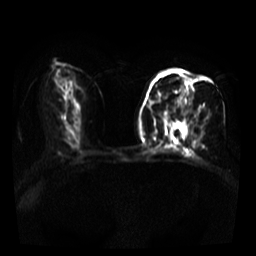
Breast MRI, one axial slice; slice 17 of 39 in the series (ordered by position); diffusion-weighted series; image 2 of 4 stored at this slice position (different b-values; order by instance number); 3 T; 5 mm slice thickness; 256 × 256 image matrix, field of view 320 × 320 mm. Female patient.
Outlined on this slice (outlined manually by an expert reader):
- tumour on diffusion-weighted imaging: bounding box [x1, y1, x2, y2] px = [189, 81, 193, 98]